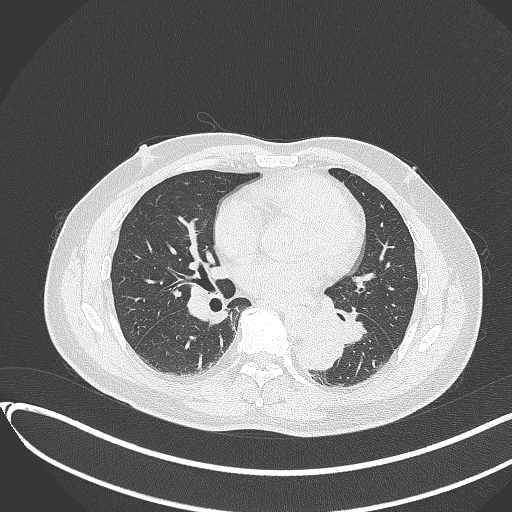
Chest CT, one axial slice; slice 159 of 417 in the series (ordered by position); reconstruction kernel B70f; 120 kVp; lung window (W 1500 / L -600 HU); 1 mm slice thickness; 512 × 512 image matrix, field of view 400 × 400 mm. Male patient, age 54 years. Case-level facts recorded for this patient, not image findings: clinical TNM (as recorded): T3 N0 M0.
Outlined on this slice (bounding box drawn by a radiologist):
- lung tumour (recorded histology: squamous cell carcinoma): bounding box [x1, y1, x2, y2] px = [294, 328, 348, 374]